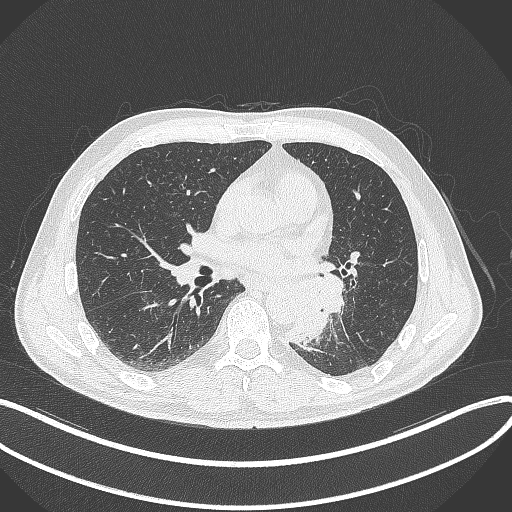
Chest CT, one axial slice. Slice 164 of 329 in the series (ordered by position). Reconstruction kernel B70f. 120 kVp. Lung window (W 1500 / L -600 HU). 1 mm slice thickness. 512 × 512 image matrix, field of view 400 × 400 mm. Patient: male, 59 years. Case-level facts recorded for this patient, not image findings: clinical TNM (as recorded): T2a N2 M0.
Annotated regions visible in this slice (bounding box drawn by a radiologist):
- lung tumour (recorded histology: squamous cell carcinoma): bounding box [x1, y1, x2, y2] px = [282, 272, 343, 346]